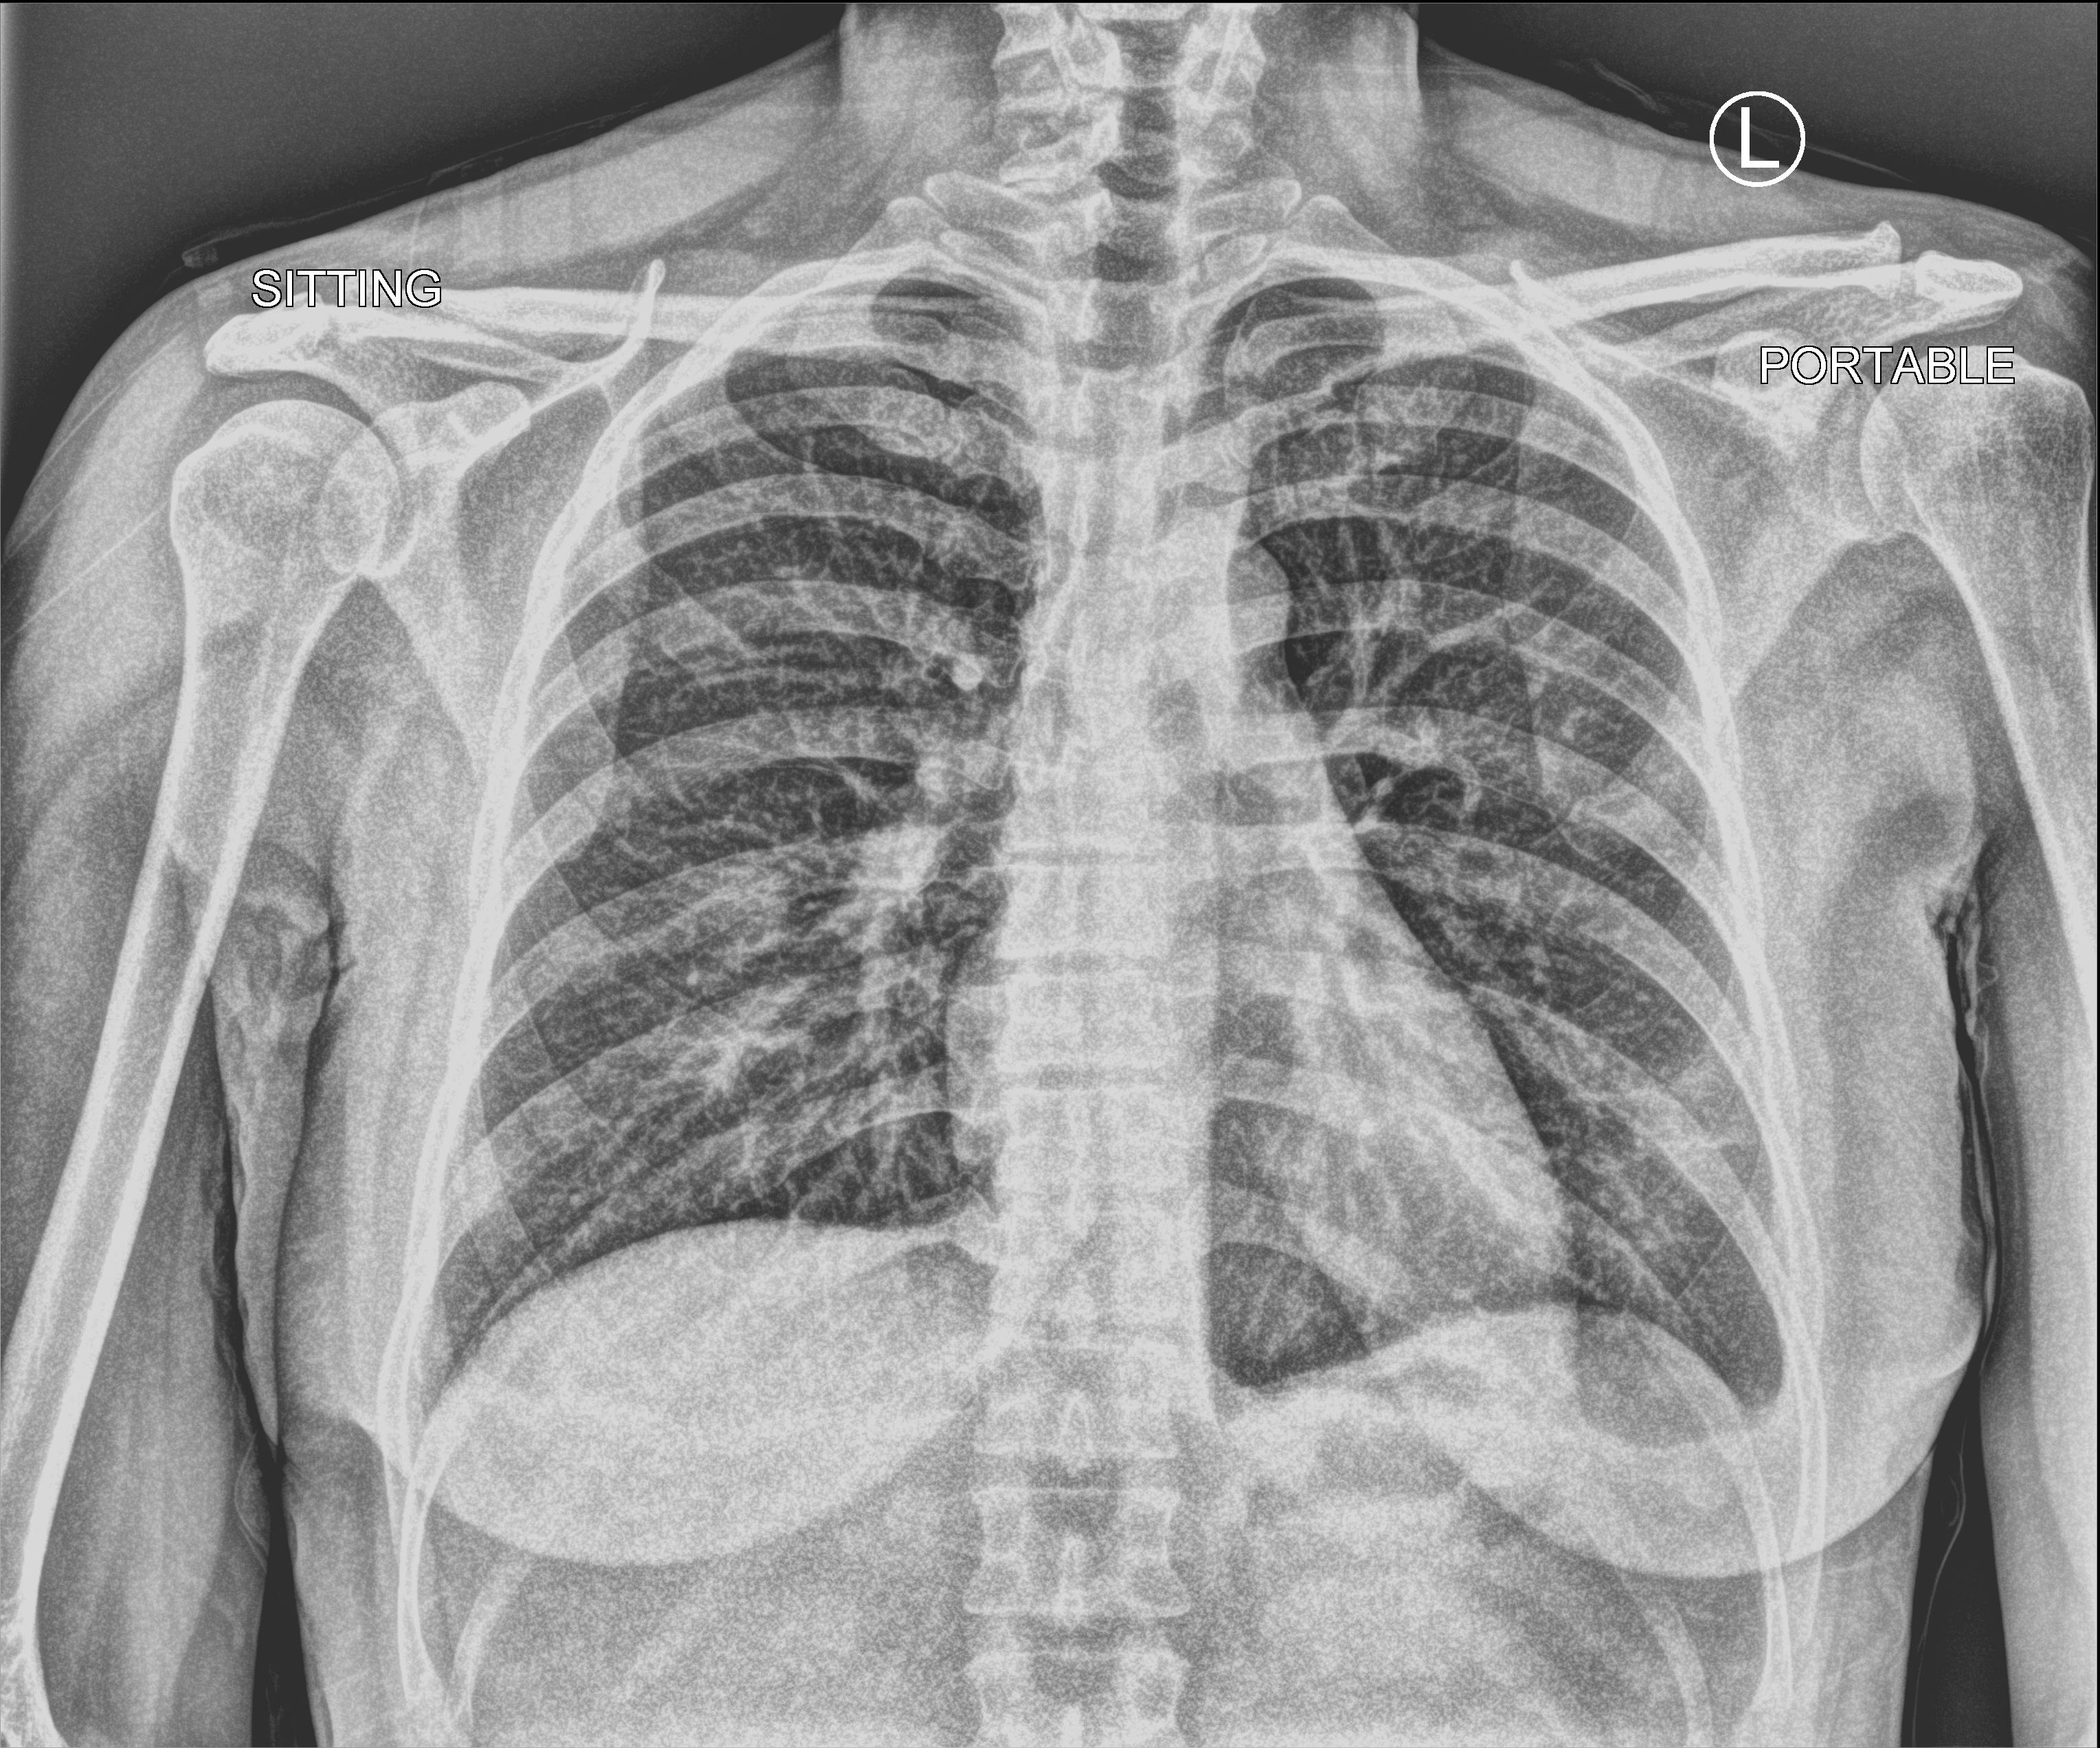
Portable chest radiograph, anteroposterior (AP) projection. Female patient hospitalised with COVID-19, age 18–59 years.
Hospital-stay facts (about this admission, not read from this image; timing relative to this image not recorded):
- mechanically ventilated during this hospital stay: no